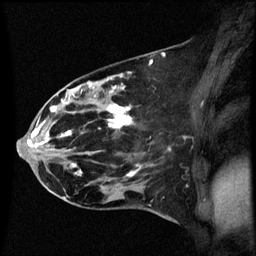
Breast MRI (dynamic contrast-enhanced), one sagittal slice. Slice 27 of 60 in the series (ordered by position). Dynamic contrast-enhanced series, image 2 of 3 at this slice position (ordered by acquisition). 1.5 T. TE 4.2 ms, TR 8.9 ms. 256 × 256 image matrix. Patient: female, 44 years. From the clinical record (not read from this slice): setting: breast cancer imaged before/during neoadjuvant chemotherapy; receptor status: HR-positive, HER2-negative.
Outlined on this slice (semi-automatic segmentation, software-assisted and operator-edited):
- analysis volume of interest (the breast-tissue region the enhancement analysis was run in; not a lesion): bounding box (x1, y1, x2, y2) in pixels: (43, 78, 153, 189)
- tumour enhancement mask (voxels above the 70 % enhancement threshold inside the analysis volume of interest): (51, 88, 135, 177)